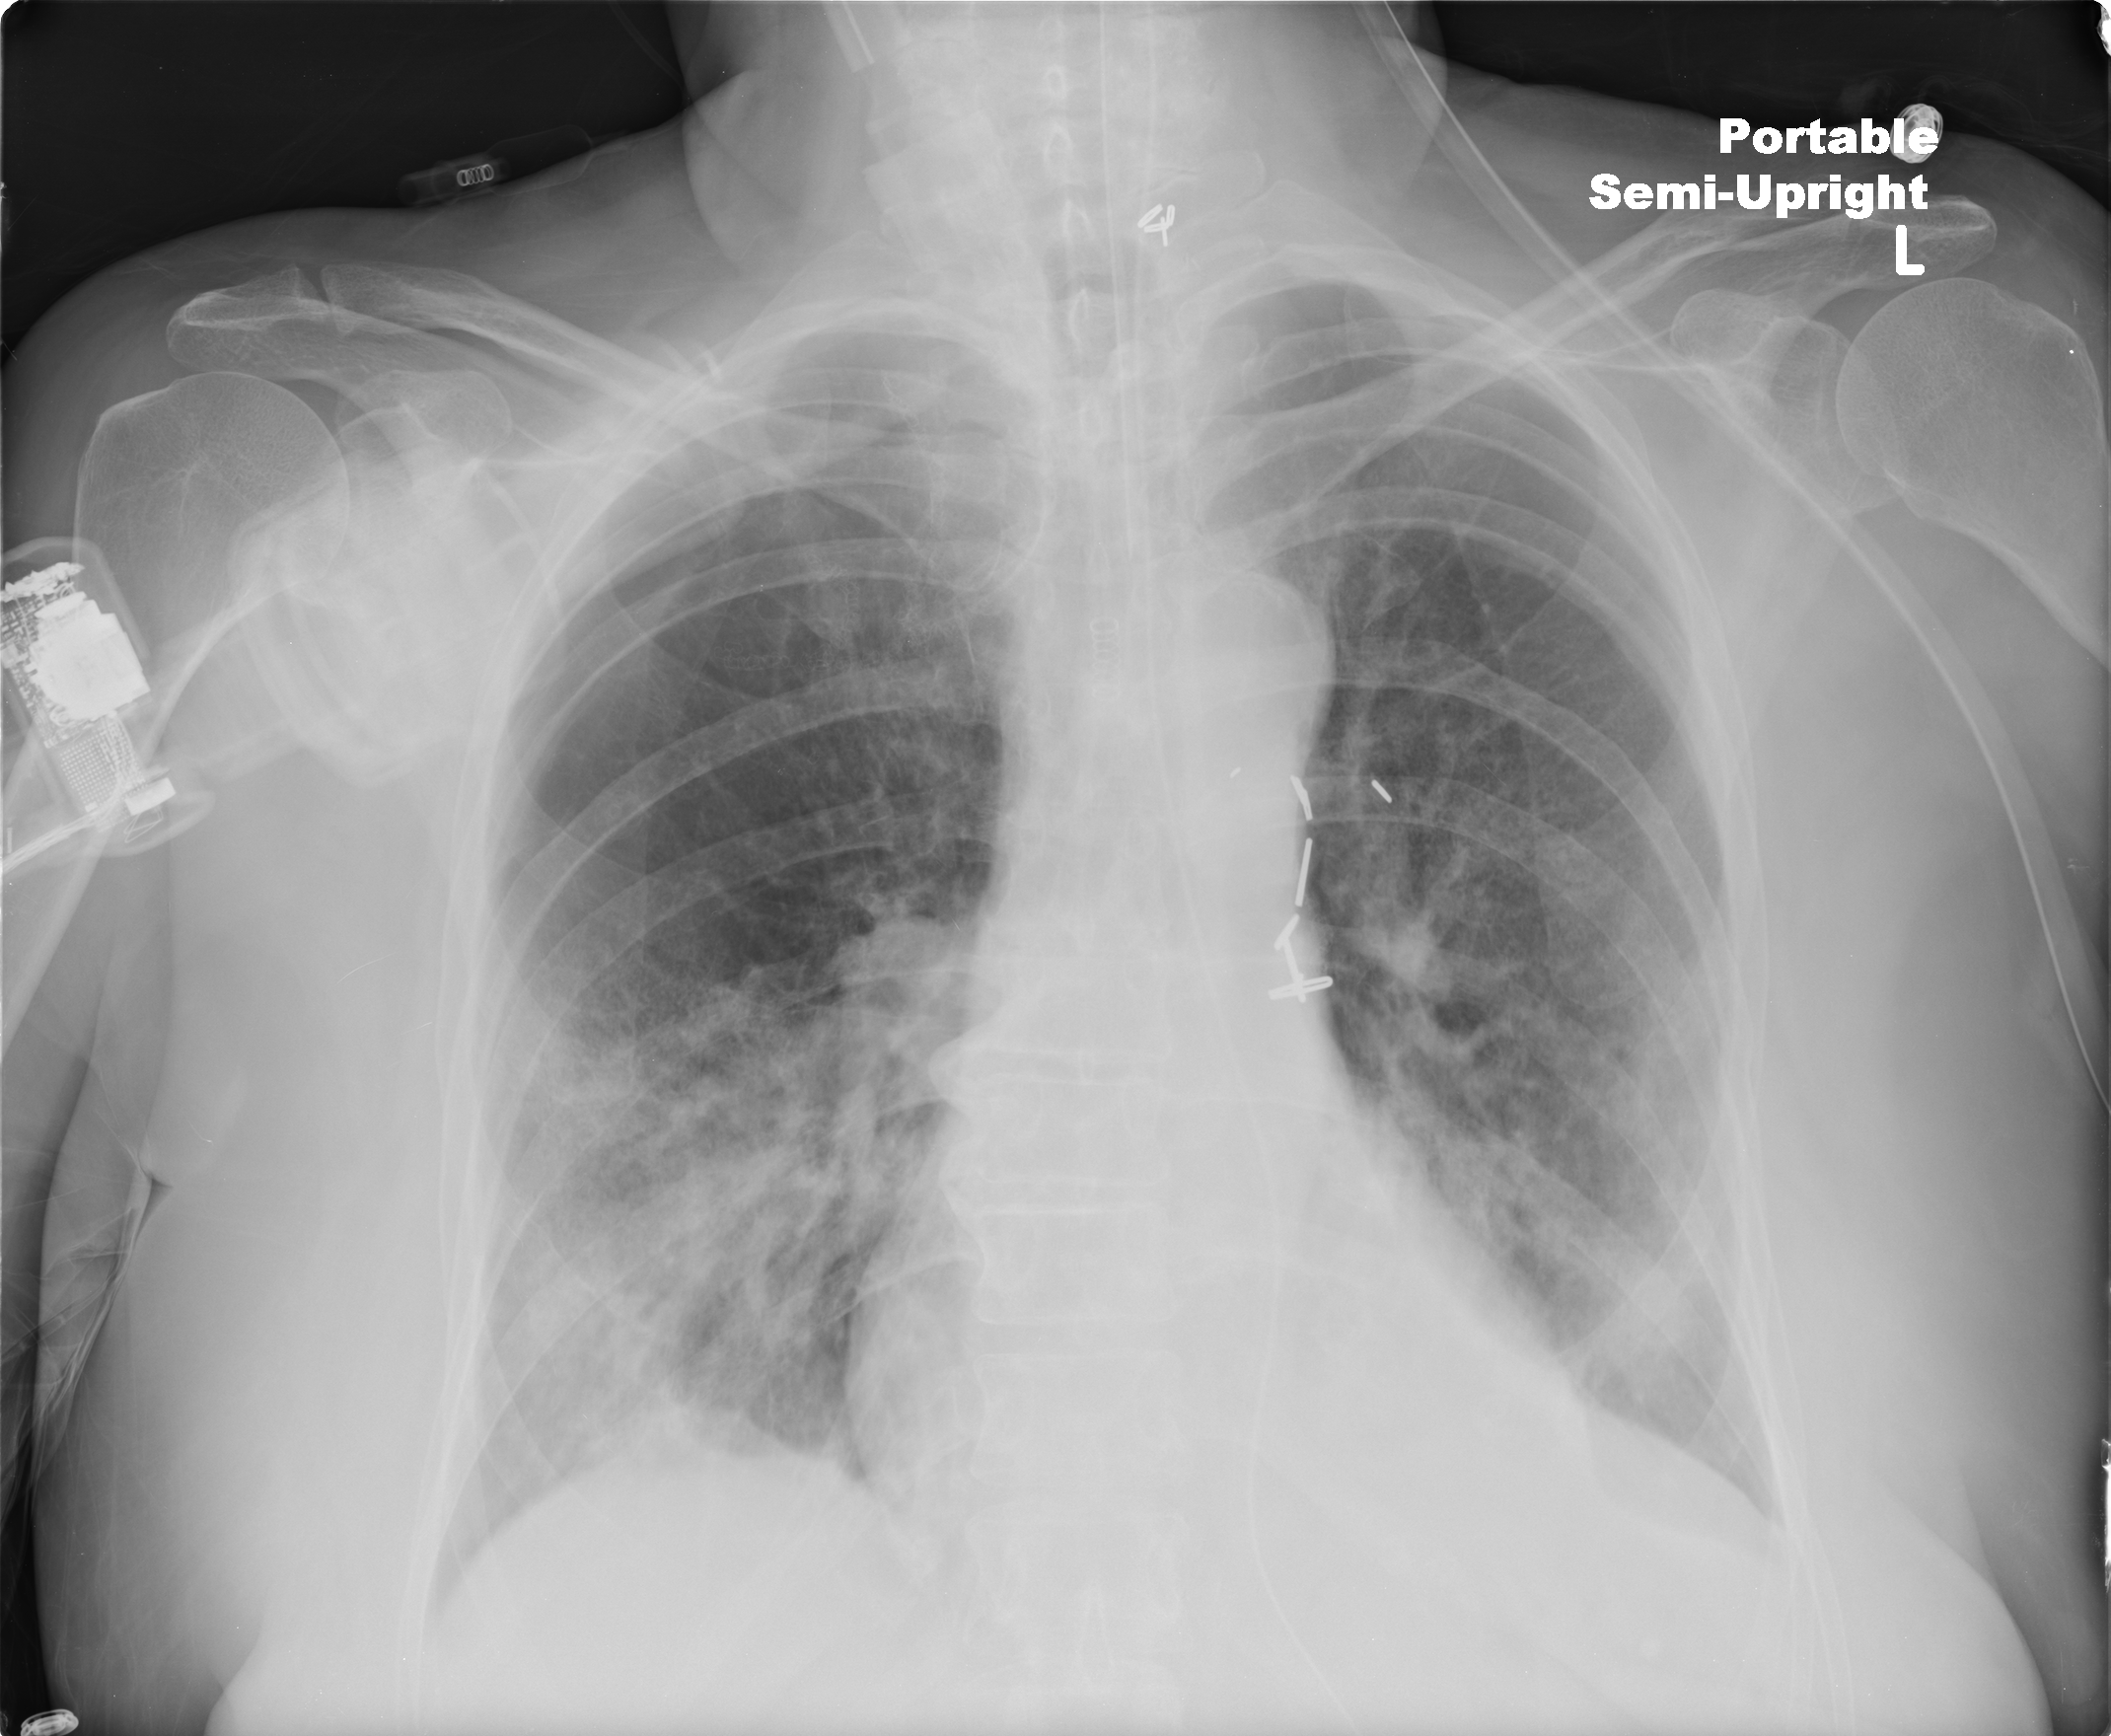
Portable chest radiograph, AP projection. Female patient, age 72 years; COVID-19 (test-positive).
Radiologist key findings (as recorded): worsening of bilateral lower lobe opacities consistent with airspace disease, much more dense in the retrocardiac left lower lobe, consistent with consolidation.